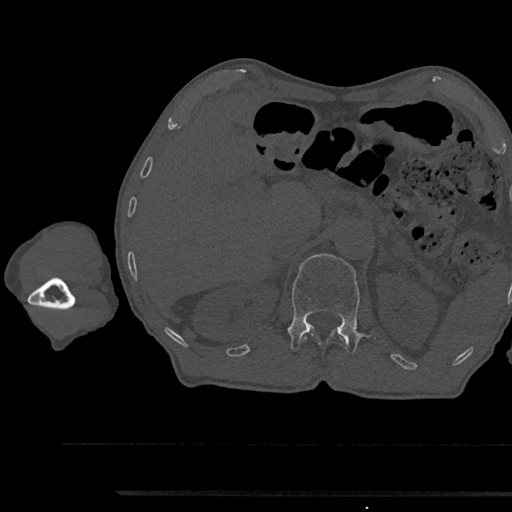
CT including the spine, one axial slice; position 664 of 797 along the scan axis; bone window (W 1800 / L 400 HU); 0.5 mm slice thickness; 512 × 512 image matrix, field of view 367 × 367 mm. Patient: male, 79 years. From the clinical record (not read from this slice): primary cancer: prostate.
Structures marked on this image (semi-automatically segmented with operator editing):
- L1 vertebra: bounding box <287,253,375,353> (left, top, right, bottom; pixels)